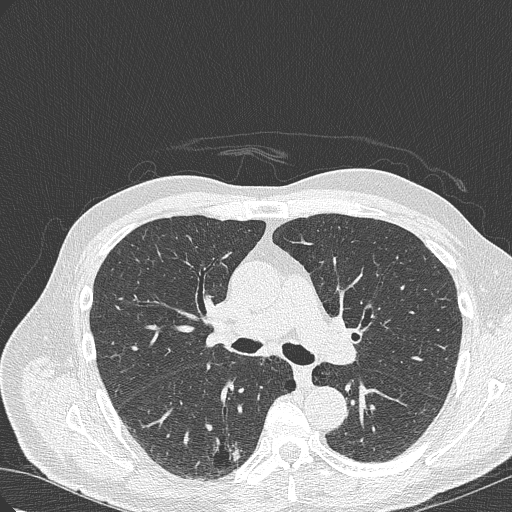
Low-dose screening chest CT, axial slice, baseline screening round, lung window (W 1500 / L -600 HU), 1 mm slice thickness, slice 124 of 322 in the series. Male, age 70 years at enrolment. Current smoker at enrolment.
Expert-annotated lung lesion, bounding box (x1, y1, x2, y2) in pixels: (200, 419, 264, 471). The screening reader recorded 4 non-calcified nodules or masses ≥4 mm on this exam (right lower lobe, right lower lobe, right upper lobe, right lower lobe); which of them this box marks is not recorded. Official screen result: positive, change unspecified: nodule(s) >= 4 mm or enlarging nodule(s), mass(es), or other non-specific abnormalities suspicious for lung cancer. Lung cancer was diagnosed 978 days after this screen (after the third annual screen): bronchiolo-alveolar adenocarcinoma, NOS, right lower lobe, poorly differentiated (G3), stage IB (AJCC 6th edition), 30 mm at pathology.